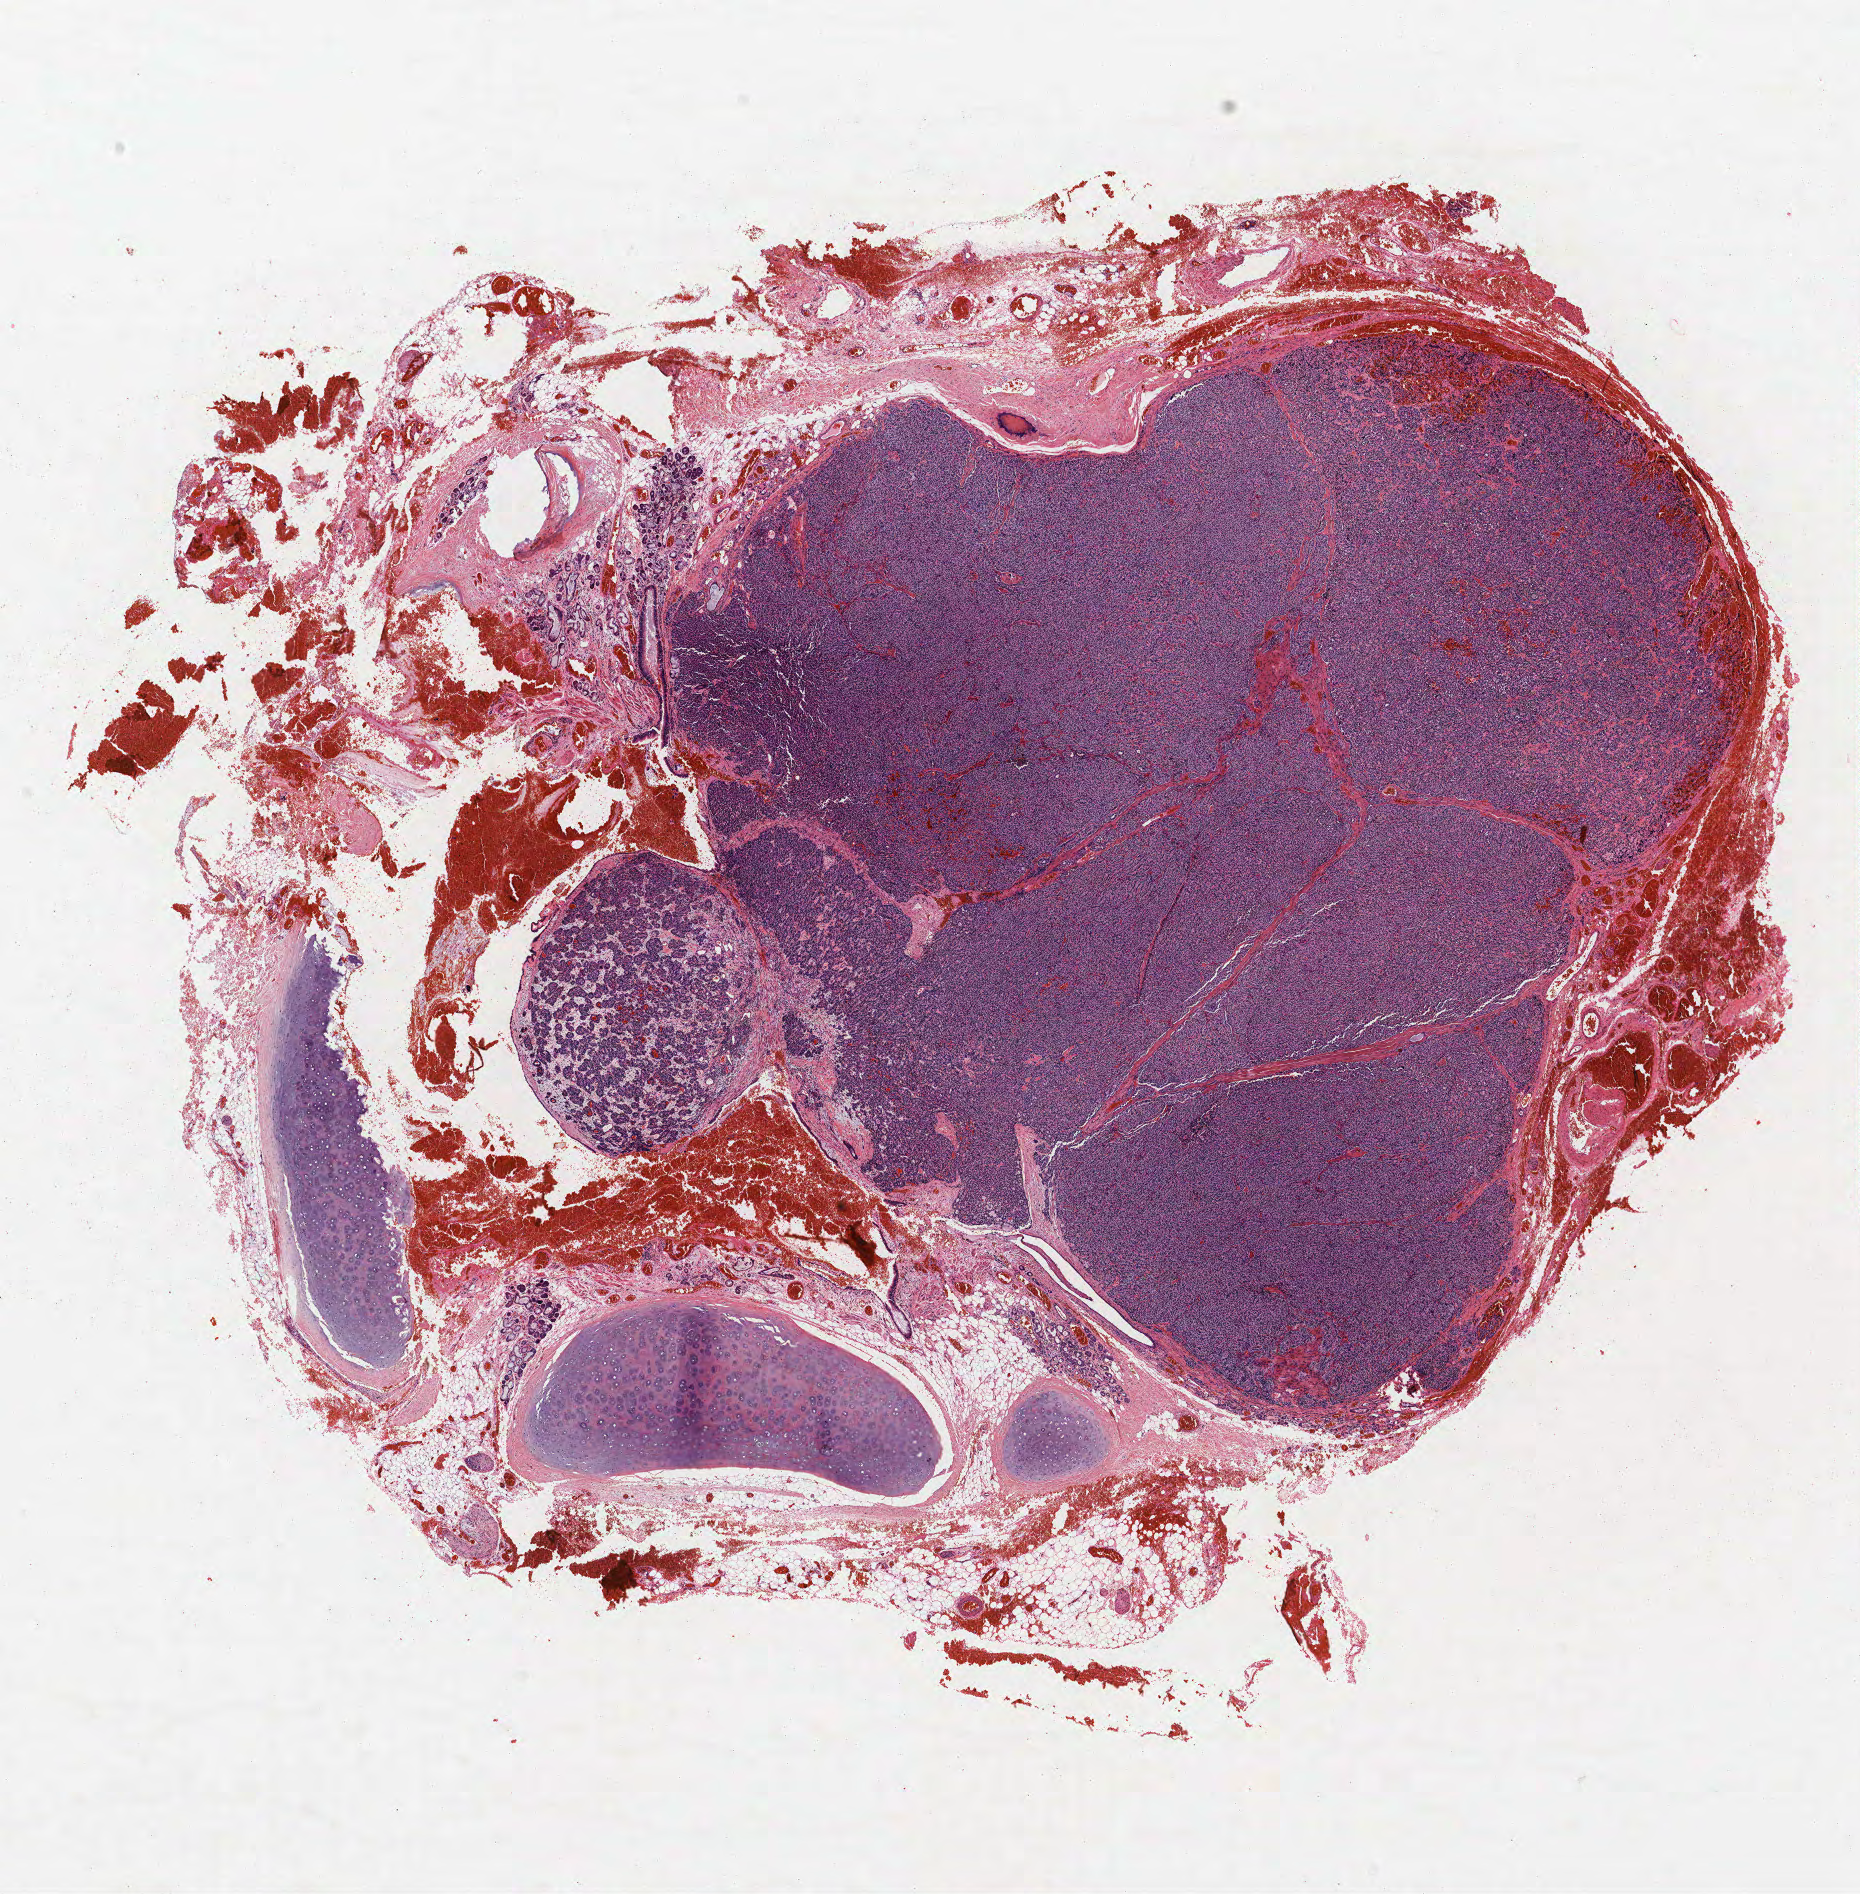
Hematoxylin and eosin (H&E) stained whole-slide image, low-resolution overview of the scanned area, about 14.9 x 15.2 mm; formalin-fixed paraffin-embedded (FFPE) section; lung. Male patient, aged 57 at enrolment.
* participant's lung-cancer diagnosis: Carcinoid tumor, NOS
* primary tumour location (clinical record): right middle lobe
* stage (AJCC 7th edition): IA
* tumour size (pathology): 15 mm